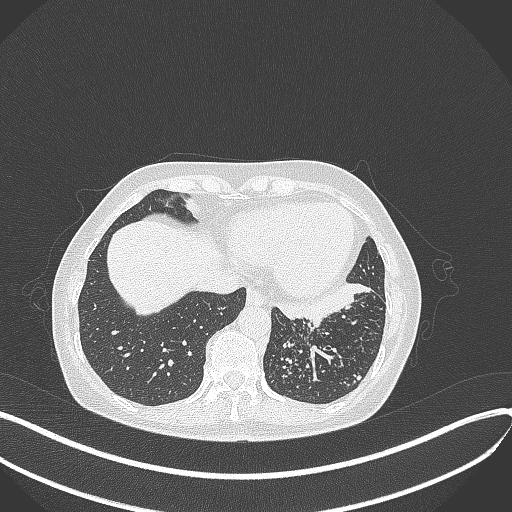
Chest CT, one axial slice. Slice 107 of 429 in the series (ordered by position). Reconstruction kernel B70f. 100 kVp. Lung window (W 1500 / L -600 HU). 1 mm slice thickness. 512 × 512 image matrix, field of view 400 × 400 mm. Female patient, age 63 years. Case-level facts recorded for this patient, not image findings: clinical TNM (as recorded): T1b N0 M0.
Outlined on this slice (bounding box drawn by a radiologist):
- lung tumour (recorded histology: adenocarcinoma): bounding box (x1, y1, x2, y2) in pixels: (269, 280, 377, 327)